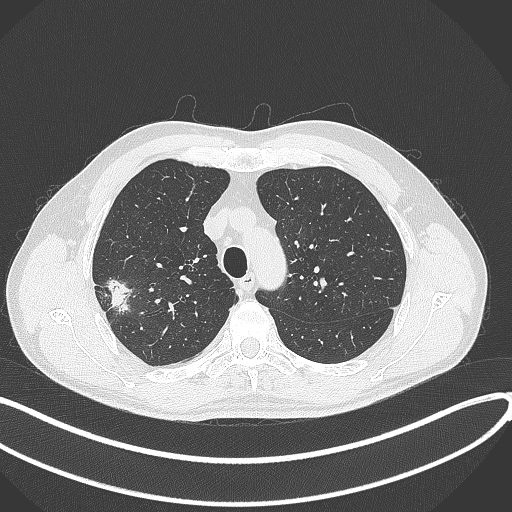
Chest CT, one axial slice. Slice 318 of 381 in the series (ordered by position). Reconstruction kernel B70f. 120 kVp. Lung window (W 1500 / L -600 HU). 1 mm slice thickness. 512 × 512 image matrix, field of view 400 × 400 mm. Patient: male, 62 years. From the clinical record (not read from this slice): clinical TNM (as recorded): T1c N0 M0.
Outlined on this slice (rectangle marked by the reading radiologist):
- lung tumour (recorded histology: adenocarcinoma): box from (x=106, y=276) to (x=134, y=314) px